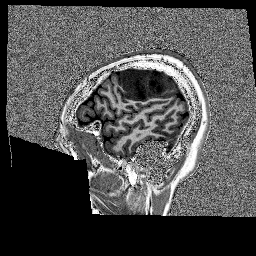
Brain MRI from a brain-tumour surgery series, one sagittal slice; slice 36 of 176 in the series (ordered by position); 1 mm slice thickness; 256 × 256 image matrix. From the clinical record (not read from this slice): histopathology: Glioblastoma; WHO grade: 4; IDH mutation: no.
Structures marked on this image (expert manual segmentation):
- tumour: bounding box [x1, y1, x2, y2] px = [118, 67, 175, 101]